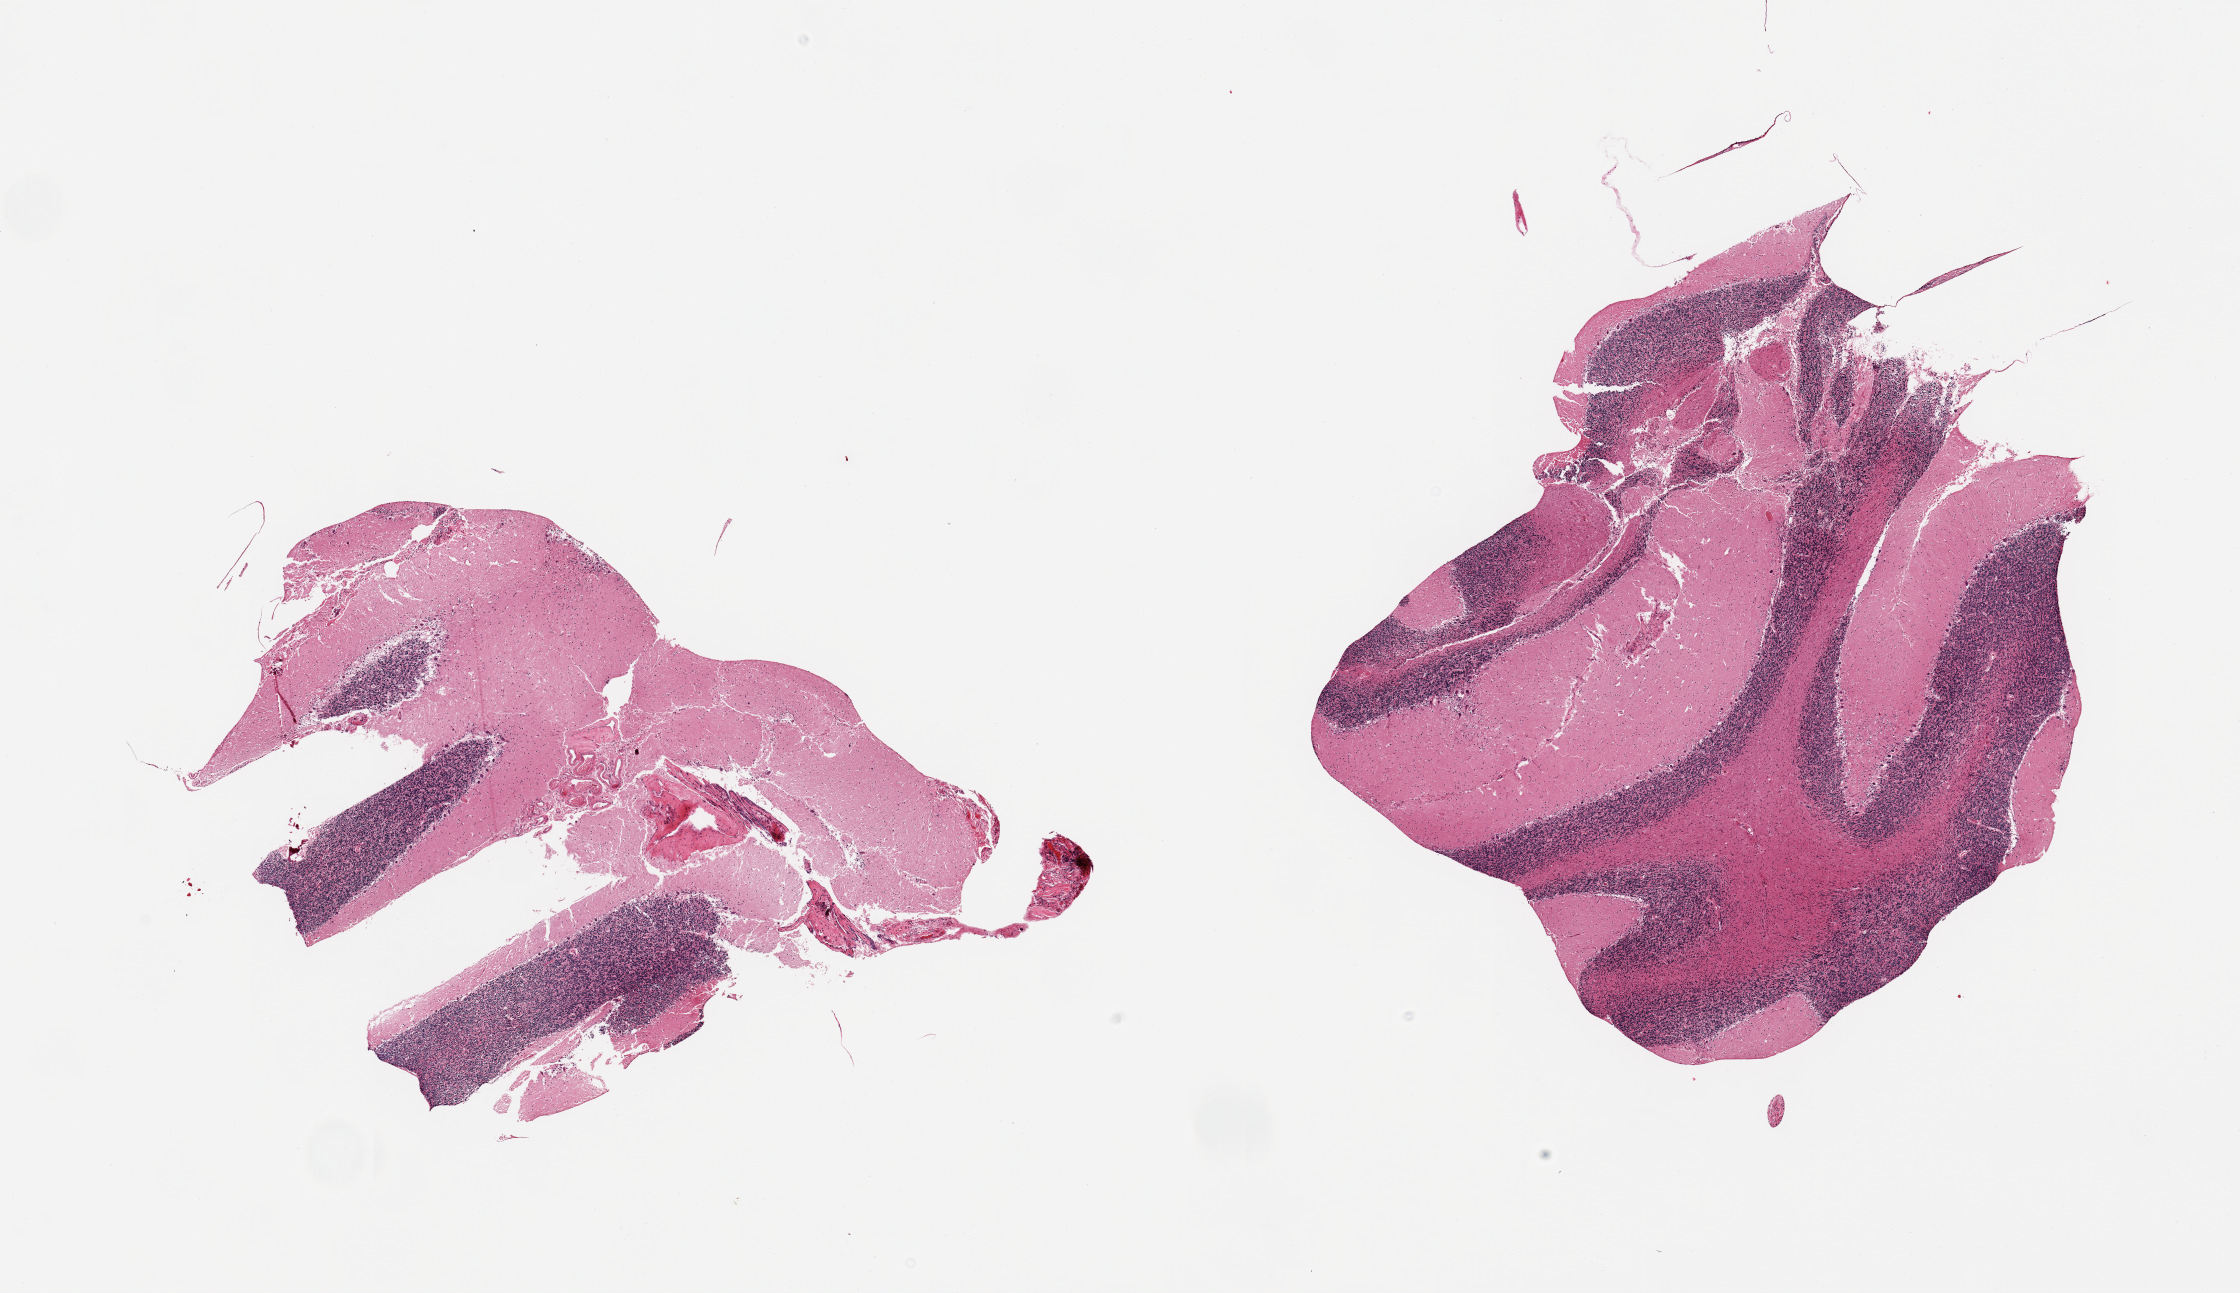
Haematoxylin and eosin whole-slide image, low-resolution overview of the scanned area, about 17.7 x 10.2 mm; PAXgene-fixed paraffin-embedded (PFPE) section; target tissue: cerebellum; tissue donor sample. Male donor.
* pathologist's review note for this sample: 2 pieces